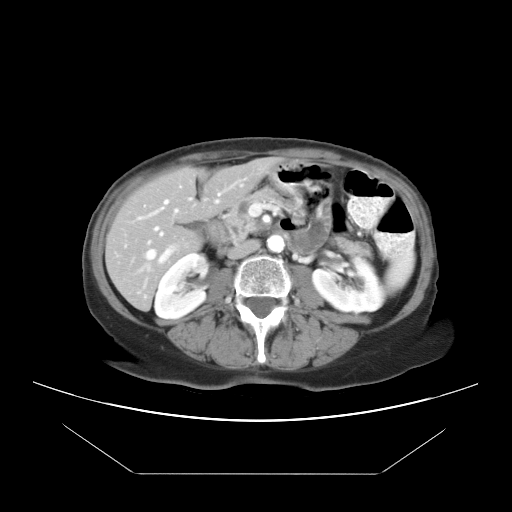
Contrast-enhanced abdominal CT, one axial slice; reconstruction kernel STANDARD; intravenous contrast given; soft-tissue window (W 400 / L 40 HU); 512 × 512 image matrix, field of view 392 × 392 mm. Female patient, age 72 years. Case-level facts recorded for this patient, not image findings: diagnosis: colorectal cancer liver metastases, imaged before liver resection; multiple liver metastases: yes; largest metastasis: 4 cm.
Outlined on this slice (manually delineated by an expert):
- hepatic veins: bounding box (x1, y1, x2, y2) in pixels: (137, 199, 179, 288)
- liver: (107, 159, 273, 308)
- planned liver remnant (the part of the liver to remain after resection): (107, 159, 273, 291)
- portal vein (with intrahepatic branches): (147, 192, 221, 262)